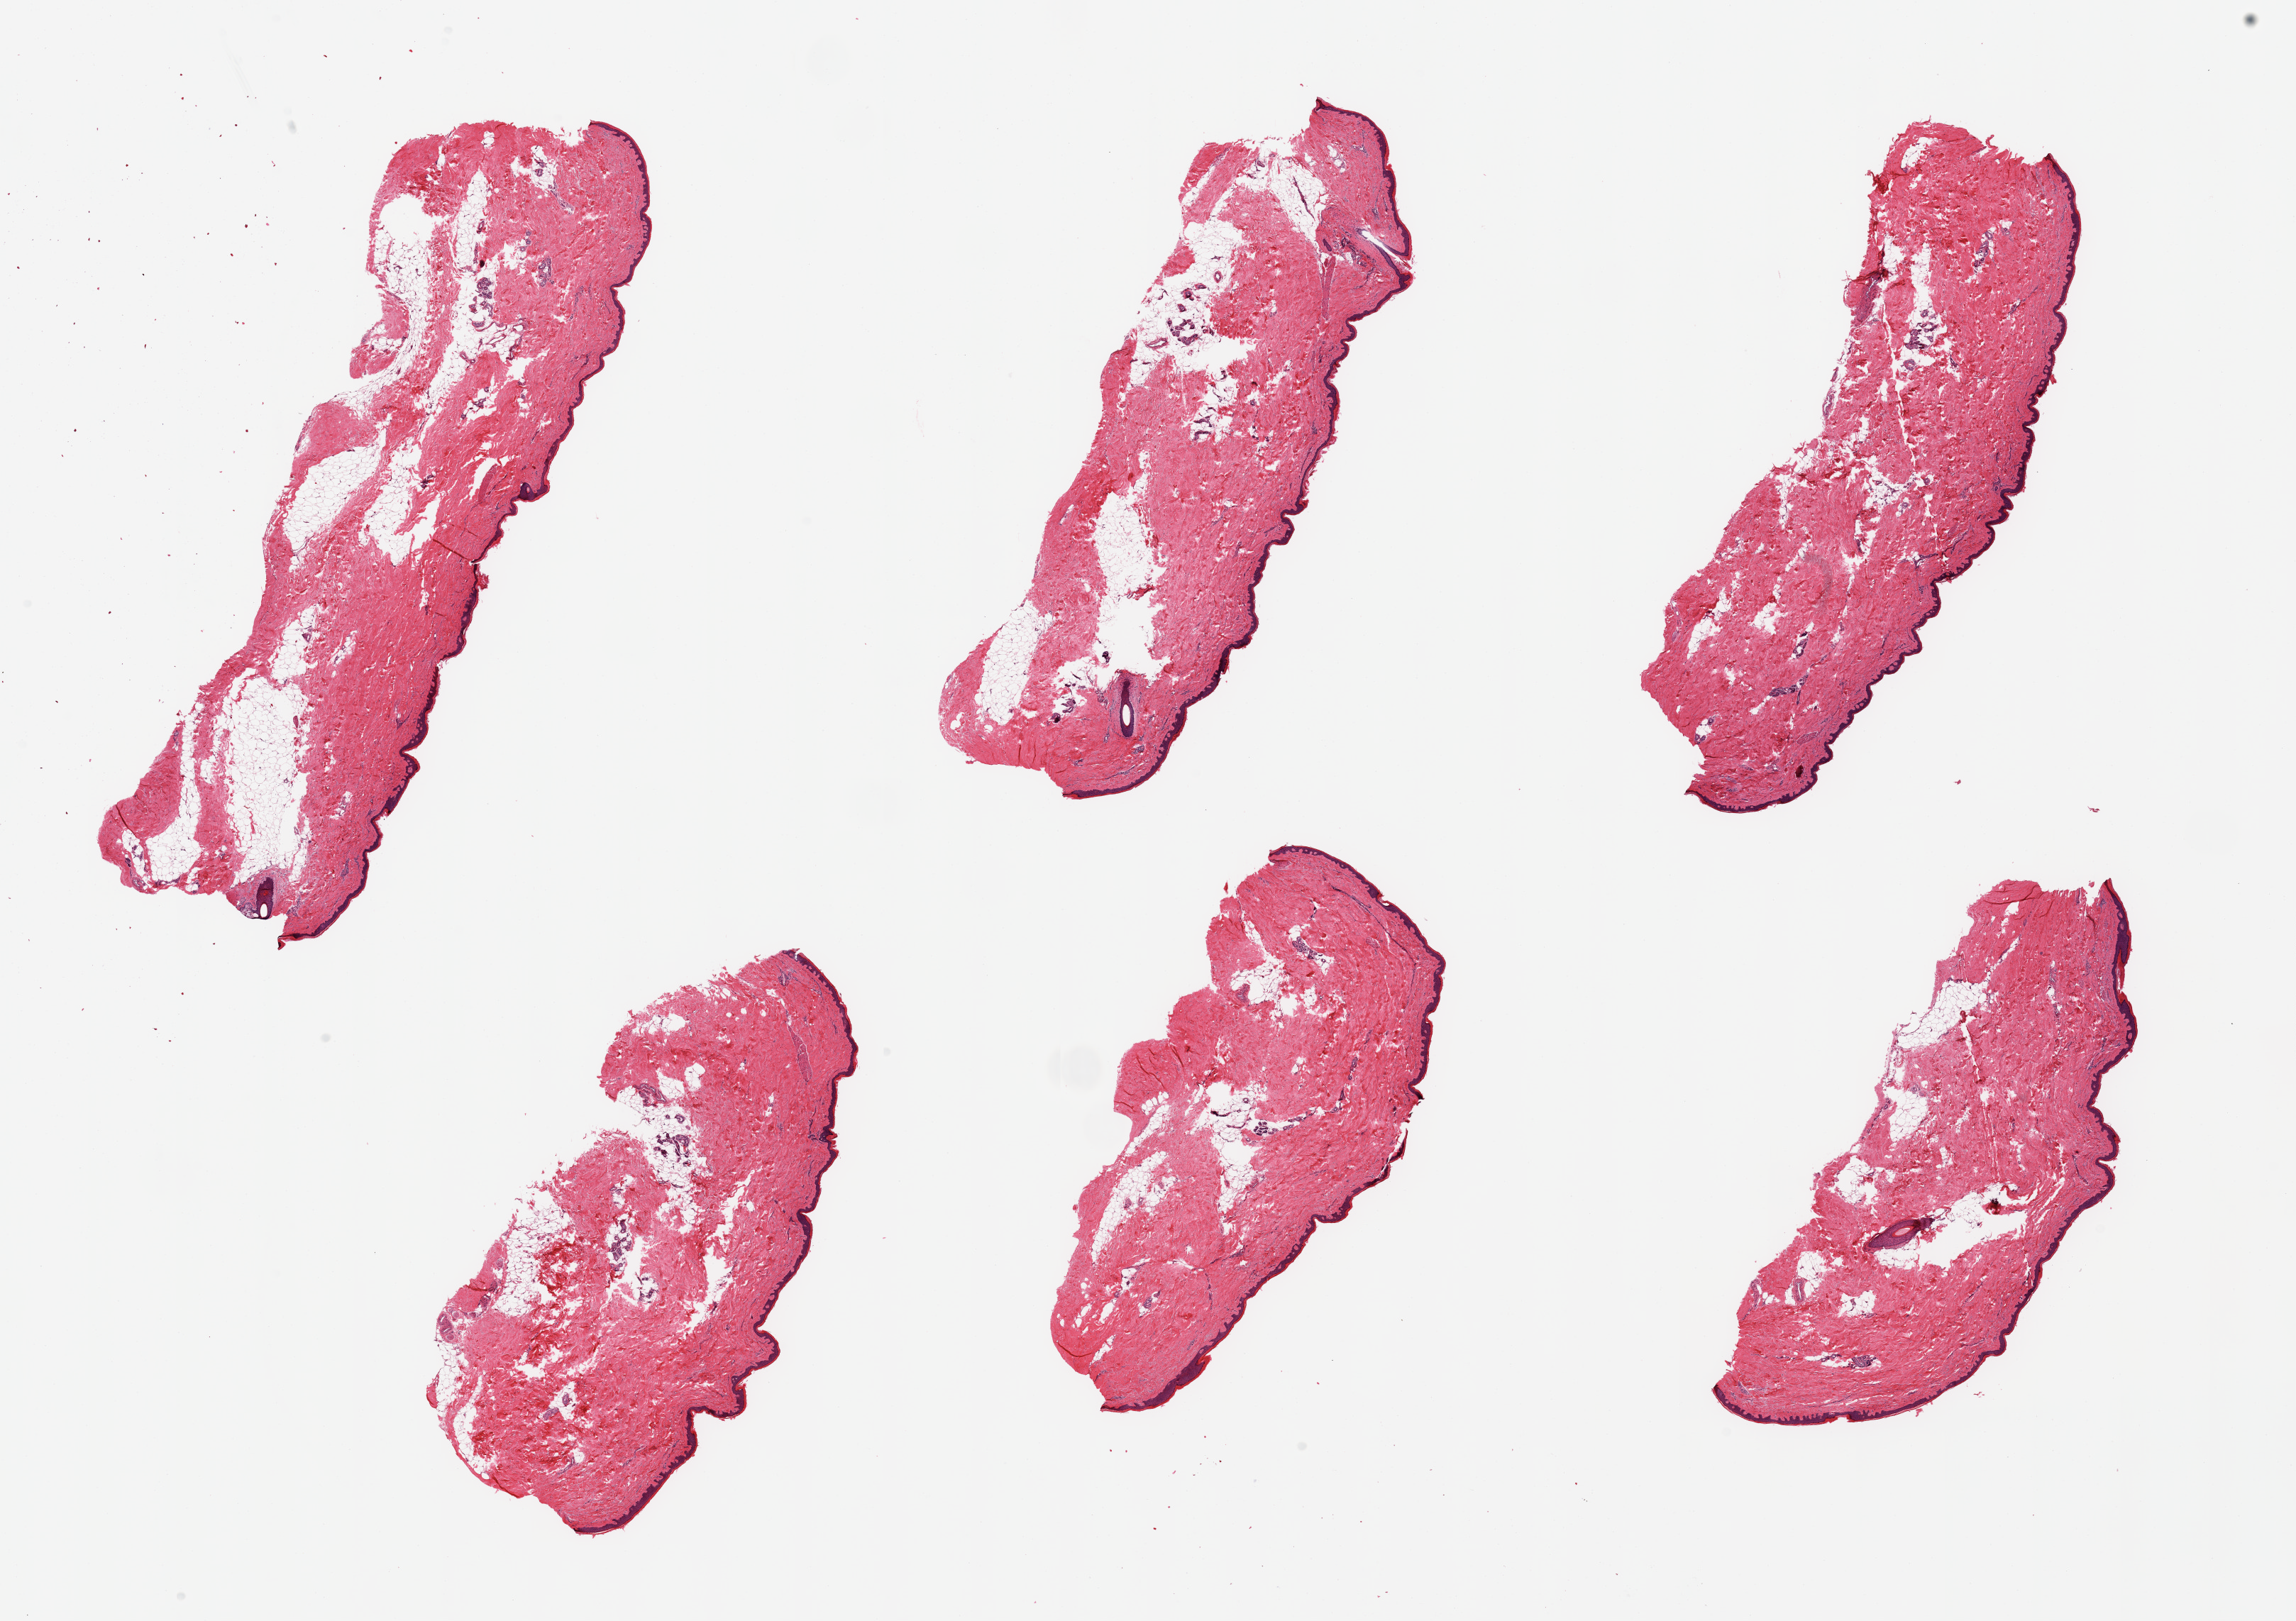
Digitized hematoxylin and eosin (H&E)-stained section, low-resolution overview of the scanned area, about 25.6 x 18.1 mm, PAXgene-fixed paraffin-embedded (PFPE) section, sampled site (target tissue): skin of lower leg, donor tissue sample. Donor sex: male.
Reviewer comment on this tissue sample: 6 pieces; 10% to 20% internal/external fat; ~44 micron thick epidermis.